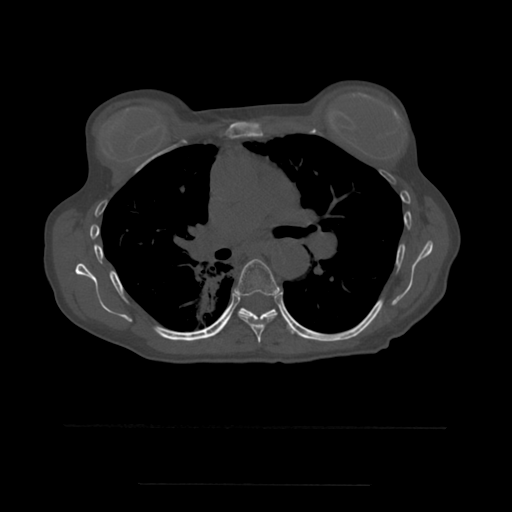
CT including the spine, one axial slice; slice 369 of 544 in the series (ordered by position); bone window (W 1800 / L 400 HU); 1.25 mm slice thickness; 512 × 512 image matrix, field of view 350 × 350 mm. Patient age 58 years. Case-level facts recorded for this patient, not image findings: primary cancer: lung.
Structures marked on this image (semi-automatic segmentation, software-assisted and operator-edited):
- T6 vertebra: box from (x=234, y=259) to (x=280, y=343) px
- T7 vertebra: (x=240, y=308)–(x=289, y=328)